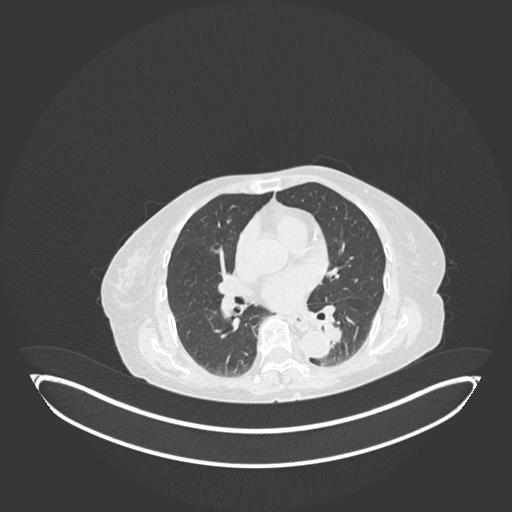
Chest CT, one axial slice. Slice 61 of 189 in the series (ordered by position). Lung window (W 1500 / L -600 HU). 512 × 512 image matrix. Patient: female, 82 years. Case-level facts recorded for this patient, not image findings: clinical TNM (as recorded): T1b N0 M1.
Outlined on this slice (bounding box drawn by a radiologist):
- lung tumour (recorded histology: adenocarcinoma): bounding box [x1, y1, x2, y2] px = [320, 321, 347, 351]